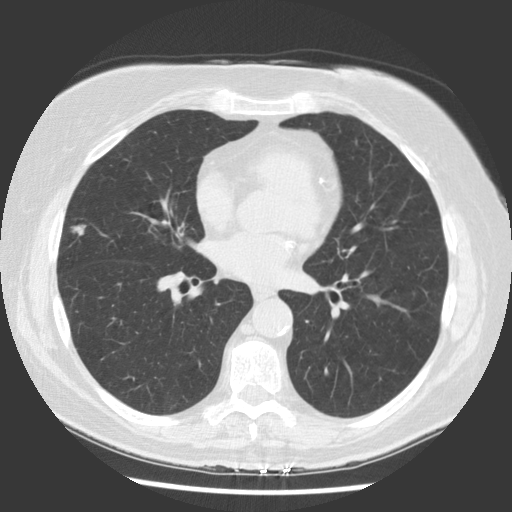
Low-dose screening chest CT, axial slice; baseline screening round; lung window (W 1500 / L -600 HU); 2.5 mm slice thickness; standard (soft-tissue) reconstruction kernel (STANDARD); slice 76 of 142 in the series. Female, age 66 years at enrolment.
Expert reader's lesion annotation, bounding box <52,212,98,252> (left, top, right, bottom; pixels). The screening reader recorded 2 non-calcified nodules or masses ≥4 mm on this exam (right middle lobe, right lower lobe); which of them this box marks is not recorded. Official screen result: positive, change unspecified: nodule(s) >= 4 mm or enlarging nodule(s), mass(es), or other non-specific abnormalities suspicious for lung cancer. Later outcome: lung cancer diagnosed 68 days after this screen — bronchiolo-alveolar carcinoma, mucinous, right middle lobe, well differentiated (G1), stage IA (AJCC 6th edition), 9 mm at pathology.